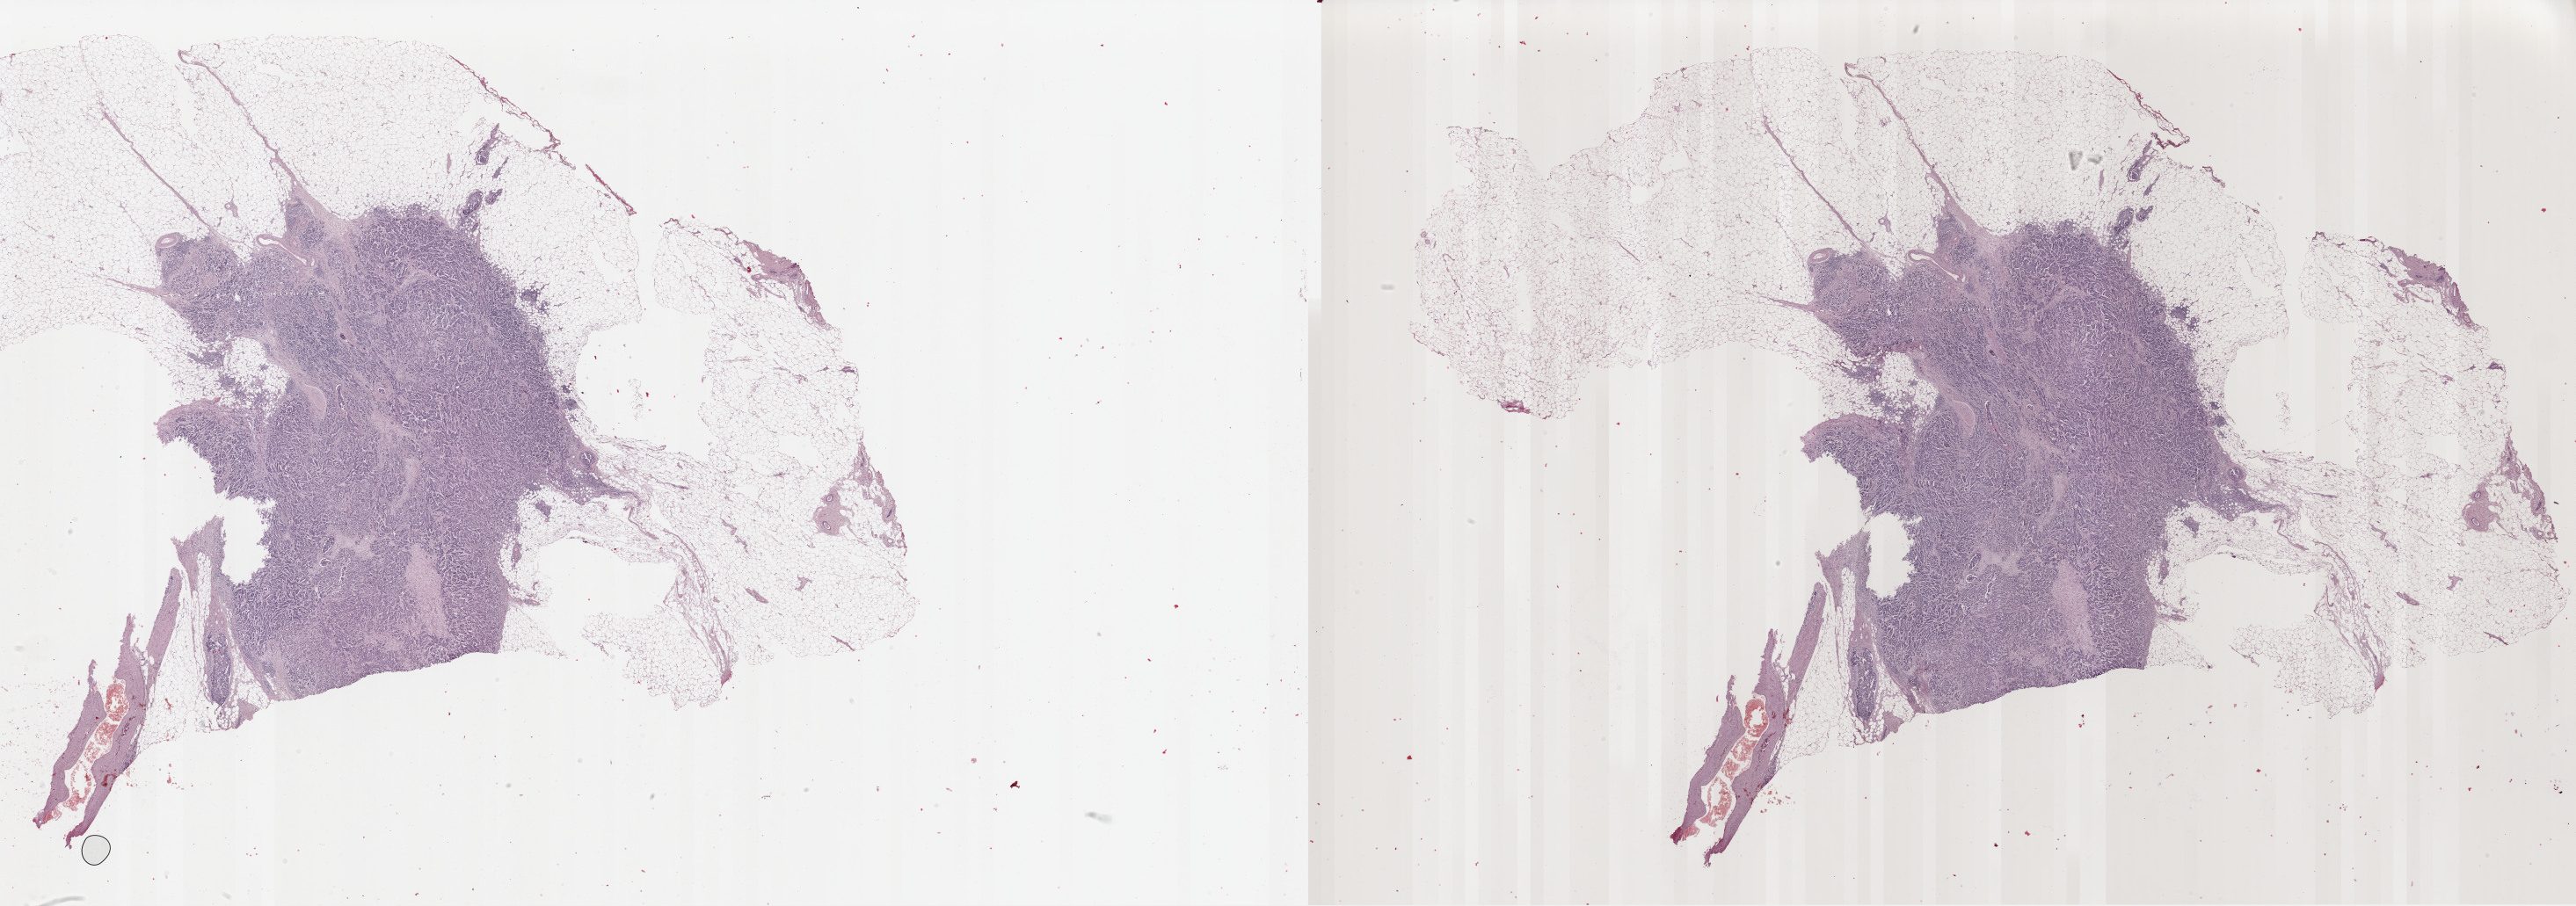
Digitized H&E-stained tissue section (whole slide) — whole scanned area (about 46.3 x 16.3 mm) shown as a low-resolution overview, formalin-fixed paraffin-embedded (FFPE) diagnostic section, breast, primary tumour sample. Patient: female, age at initial diagnosis 81 years.
• diagnosis: Infiltrating duct carcinoma, NOS
• AJCC pathologic stage: IIIA (7th edition)
• lymph nodes positive (case pathology): 6 of 14 examined